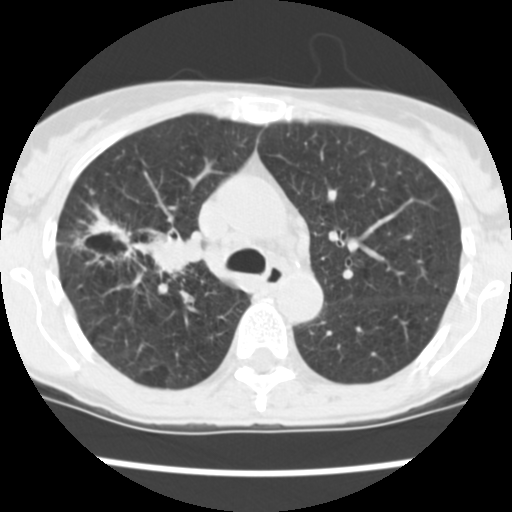
Low-dose screening chest CT, one axial slice; position 166 of 252 along the scan axis; reconstruction kernel STANDARD; 120 kVp; lung window (W 1500 / L -600 HU); 2.5 mm slice thickness; 512 × 512 image matrix, field of view 276 × 276 mm.
Annotated regions visible in this slice (outlined manually by an expert reader):
- lesion 2 (tumor, lower lobe of right lung): bounding box <87,212,204,277> (left, top, right, bottom; pixels)